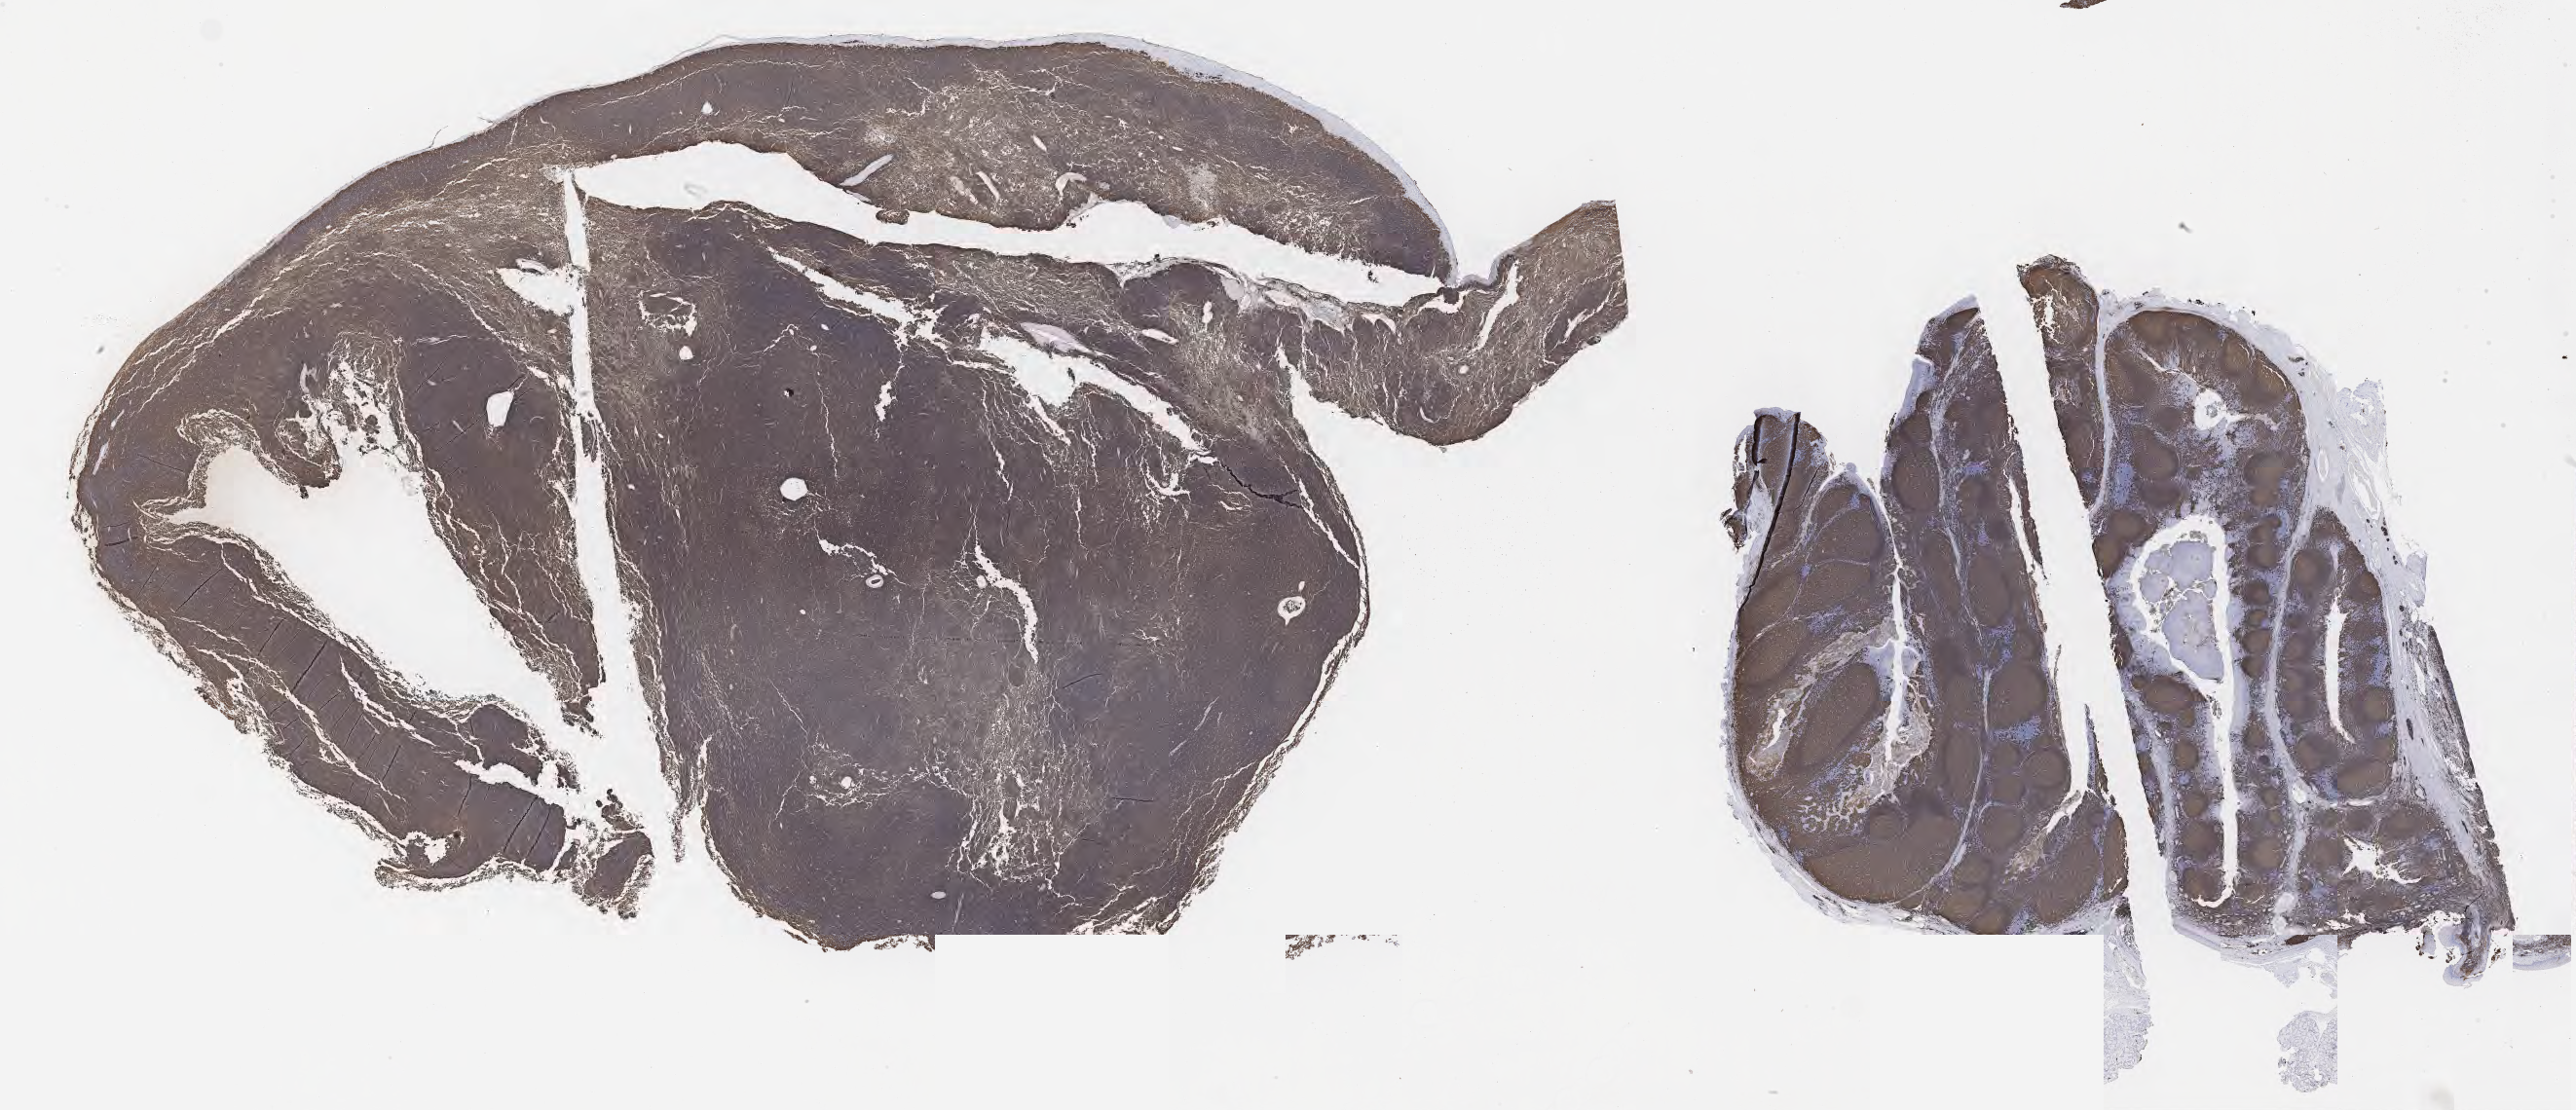
IHC for CD20, whole-slide image, a low-resolution overview of the entire scanned area, about 42.8 x 18.4 mm. Tumor tissue. Patient: female, age at initial diagnosis 3 years.
Diagnosis: Burkitt lymphoma, NOS.